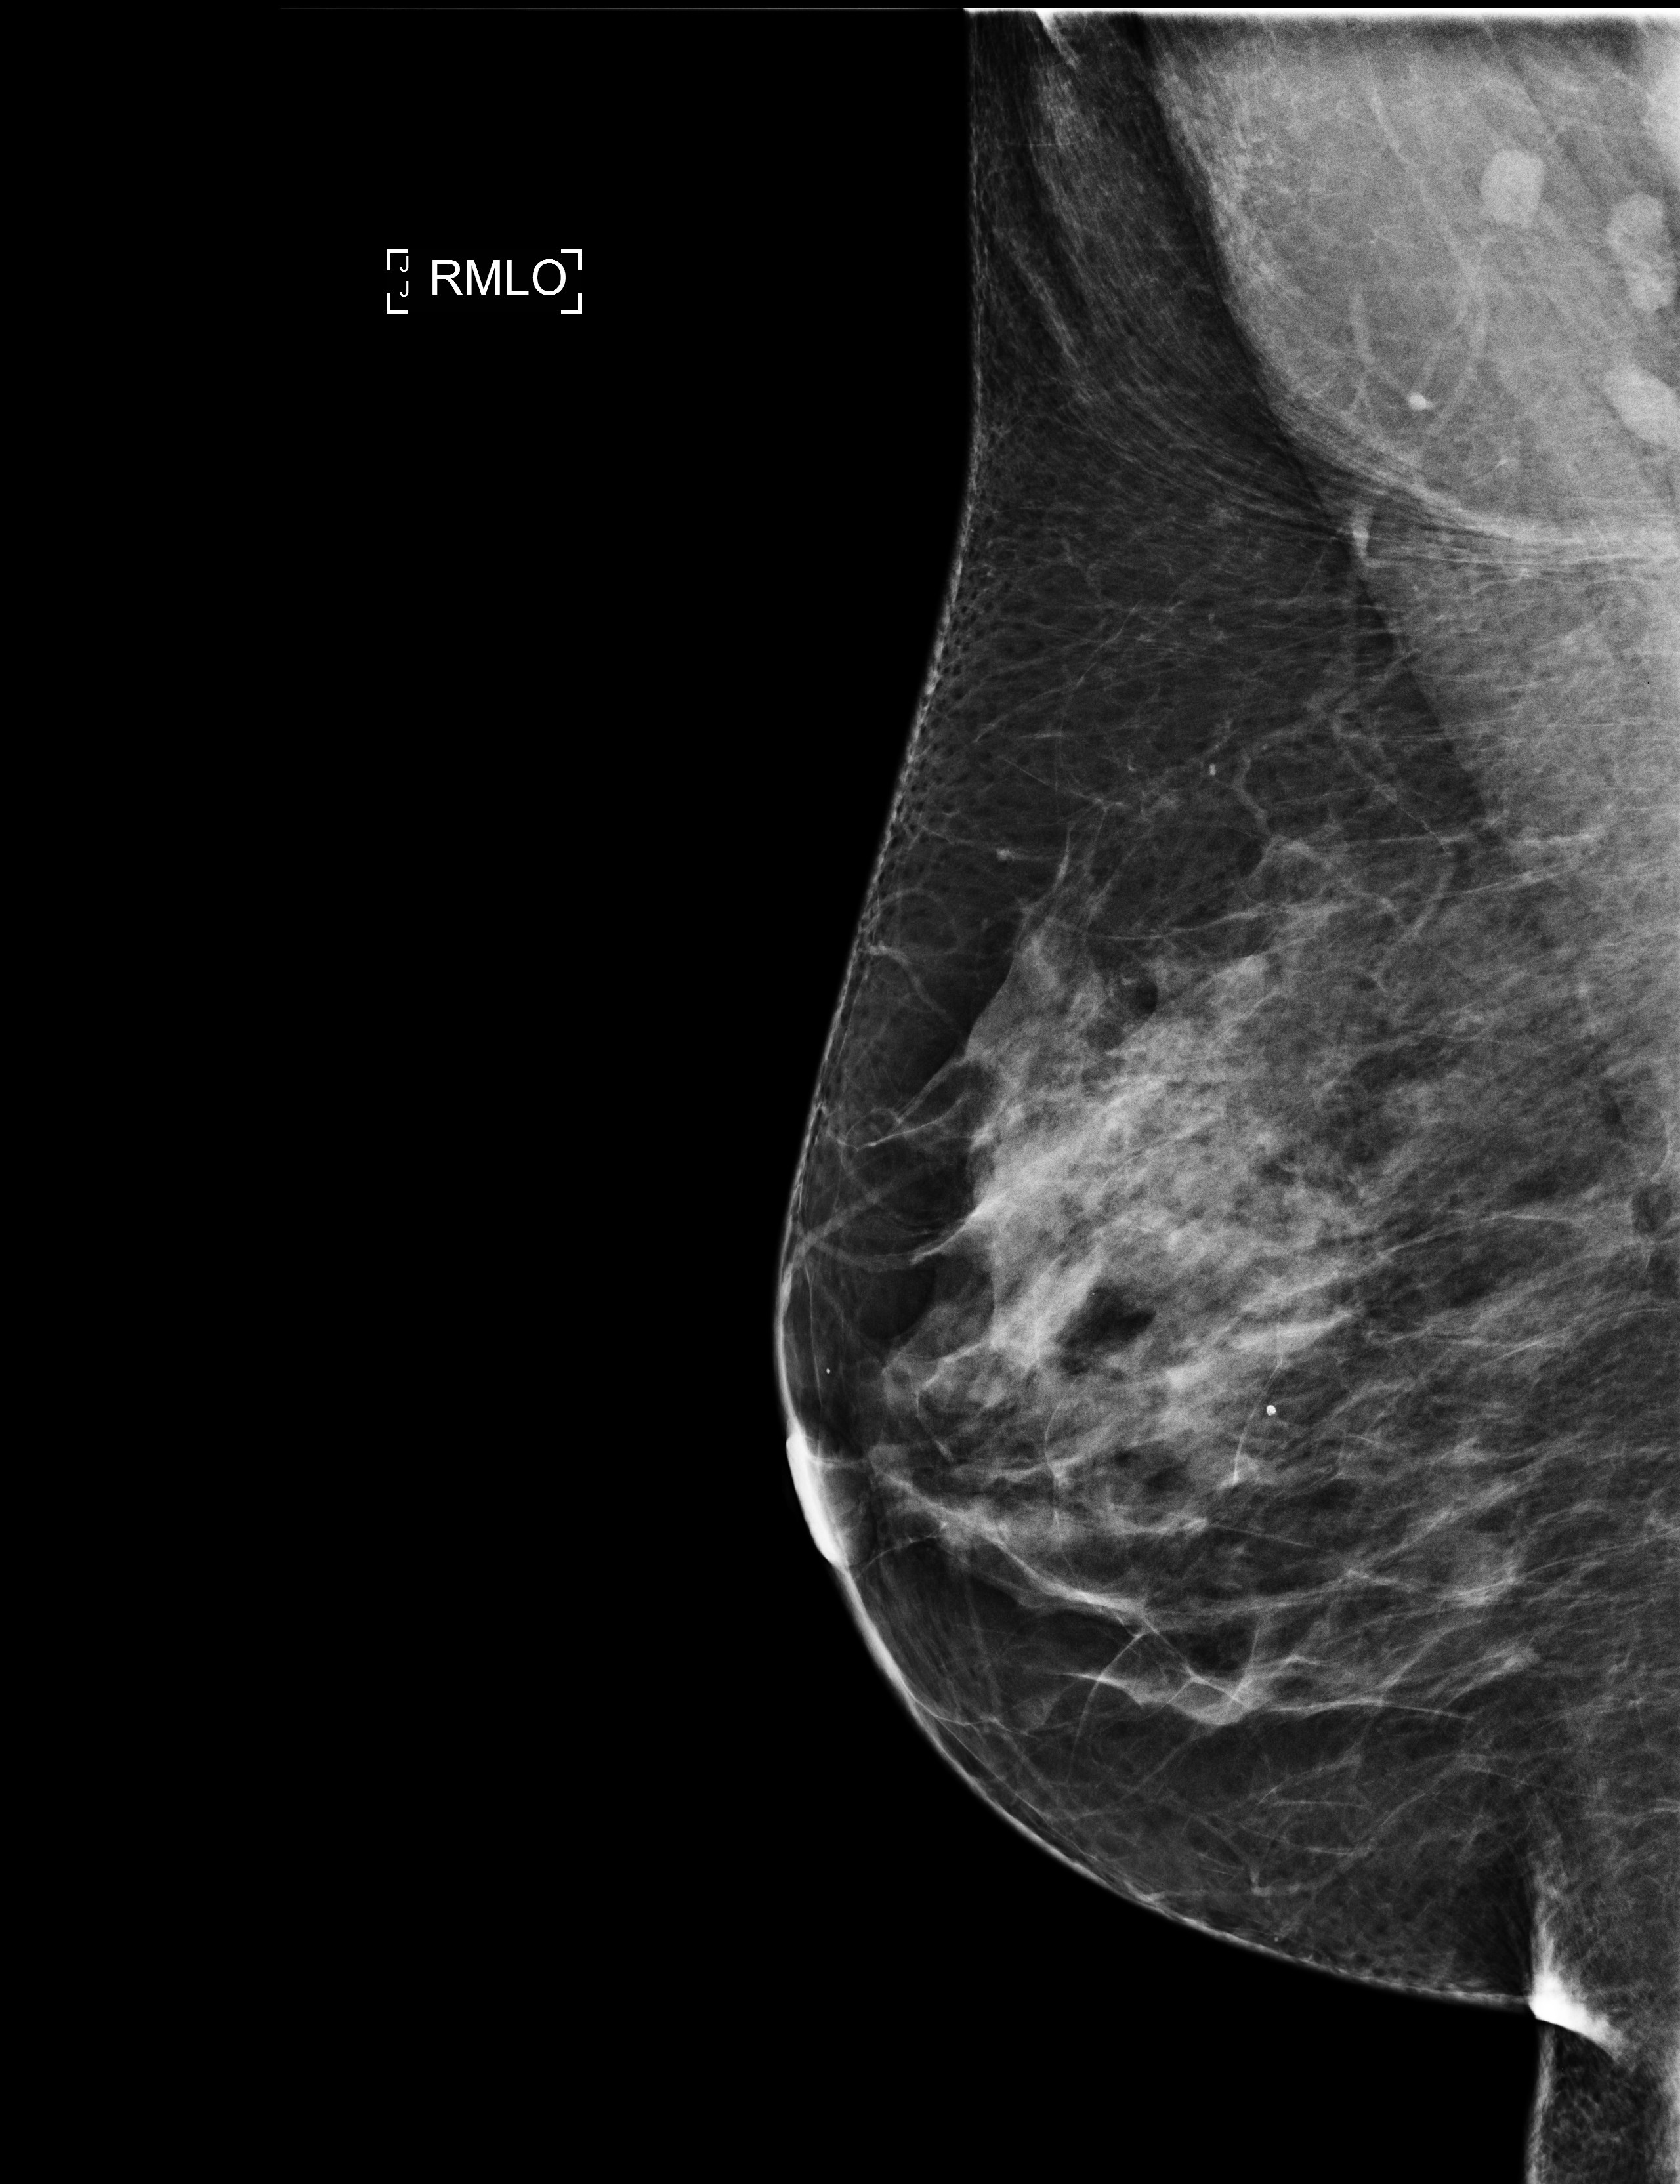
Digital mammogram (FFDM); right breast; medio-lateral oblique projection; screening examination. Patient aged 66 years (female).
- breast density at the screening exam (both breasts): heterogeneously dense (BI-RADS density category c)
- final BI-RADS assessment for this screening round (tomosynthesis exam, both breasts): category 2
- recall: no recall after this screen